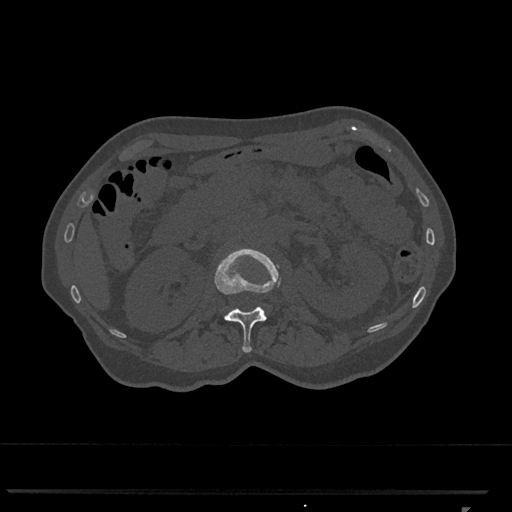
CT including the spine, one axial slice; 120 kVp; bone window (W 1800 / L 400 HU); 0.5 mm slice thickness; 512 × 512 image matrix, field of view 380 × 380 mm. Patient: female, 62 years. From the clinical record (not read from this slice): primary cancer: renal.
Annotated regions visible in this slice (semi-automatically segmented with operator editing):
- L1 vertebra: bounding box (x1, y1, x2, y2) in pixels: (214, 248, 281, 352)